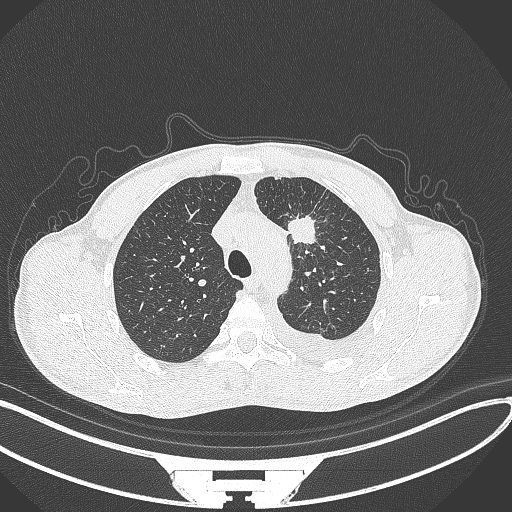
Chest CT, one axial slice; position 258 of 371 along the scan axis; reconstruction kernel B70f; 120 kVp; lung window (W 1500 / L -600 HU); 1 mm slice thickness; 512 × 512 image matrix. Male patient, age 49 years. Case-level facts recorded for this patient, not image findings: clinical TNM (as recorded): T1c N1 M1.
Structures marked on this image (rectangle marked by the reading radiologist):
- lung tumour (recorded histology: adenocarcinoma): box from (x=284, y=212) to (x=326, y=253) px